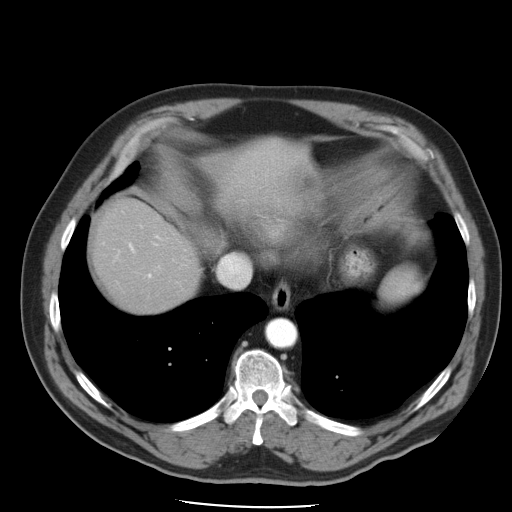
Contrast-enhanced abdominal CT, one axial slice. Slice 42 of 49 in the series (ordered by position). Reconstruction kernel STANDARD. 120 kVp. Intravenous contrast given. Soft-tissue window (W 400 / L 40 HU). 5 mm slice thickness. 512 × 512 image matrix. Male patient, age 68 years. Case-level facts recorded for this patient, not image findings: diagnosis: colorectal cancer liver metastases, imaged before liver resection; multiple liver metastases: yes; largest metastasis: 1.7 cm; disease in both lobes: no.
Structures marked on this image (outlined manually by an expert reader):
- hepatic veins: bounding box (x1, y1, x2, y2) in pixels: (218, 255, 250, 287)
- liver: (94, 200, 200, 314)
- planned liver remnant (the part of the liver to remain after resection): (94, 200, 200, 314)
- portal vein (with intrahepatic branches): (129, 236, 159, 278)